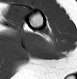
MRI of an extremity soft-tissue mass, one axial slice; position 5 of 28 along the scan axis; MR volume resampled by the dataset authors to the PET/CT grid (not the native acquisition matrix); 3.27 mm slice thickness; 77 × 79 image matrix, field of view 75 × 77 mm. Female patient. From the clinical record (not read from this slice): histological type: malignant fibrous histiocytoma; grade: low; site of the primary tumour: left arm.
Structures marked on this image (expert contour drawn on MRI and transferred to this co-registered scan by the dataset authors):
- gross tumour volume (mass): bounding box [x1, y1, x2, y2] px = [37, 38, 56, 55]